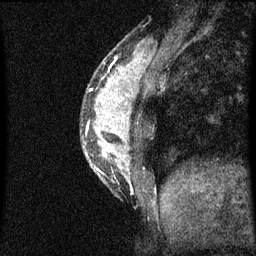
Breast MRI (dynamic contrast-enhanced), one sagittal slice; slice 19 of 60 in the series (ordered by position); dynamic contrast-enhanced series, image 2 of 3 at this slice position (ordered by acquisition); 1.5 T; TE 4.2 ms, TR 8 ms; 2 mm slice thickness; 256 × 256 image matrix. Patient: female, 33 years.
Outlined on this slice (semi-automatic segmentation, software-assisted and operator-edited):
- analysis volume of interest (the breast-tissue region the enhancement analysis was run in; not a lesion): box from (x=81, y=56) to (x=151, y=195) px
- tumour enhancement mask (voxels above the 70 % enhancement threshold inside the analysis volume of interest): (x=86, y=68)–(x=133, y=191)